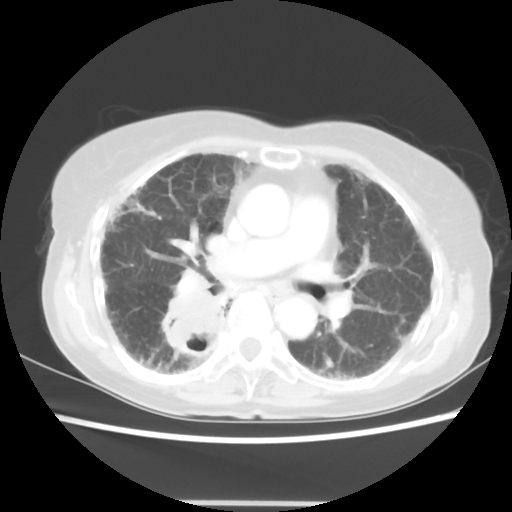
Chest CT, one axial slice; slice 29 of 52 in the series (ordered by position); reconstruction kernel STANDARD; 120 kVp; lung window (W 1500 / L -600 HU); 5 mm slice thickness; 512 × 512 image matrix, field of view 325 × 325 mm. Female patient, age 71 years. Case-level facts recorded for this patient, not image findings: clinical TNM (as recorded): T3 N0 M0.
Structures marked on this image (rectangle marked by the reading radiologist):
- lung tumour (recorded histology: squamous cell carcinoma): box from (x=154, y=283) to (x=228, y=366) px